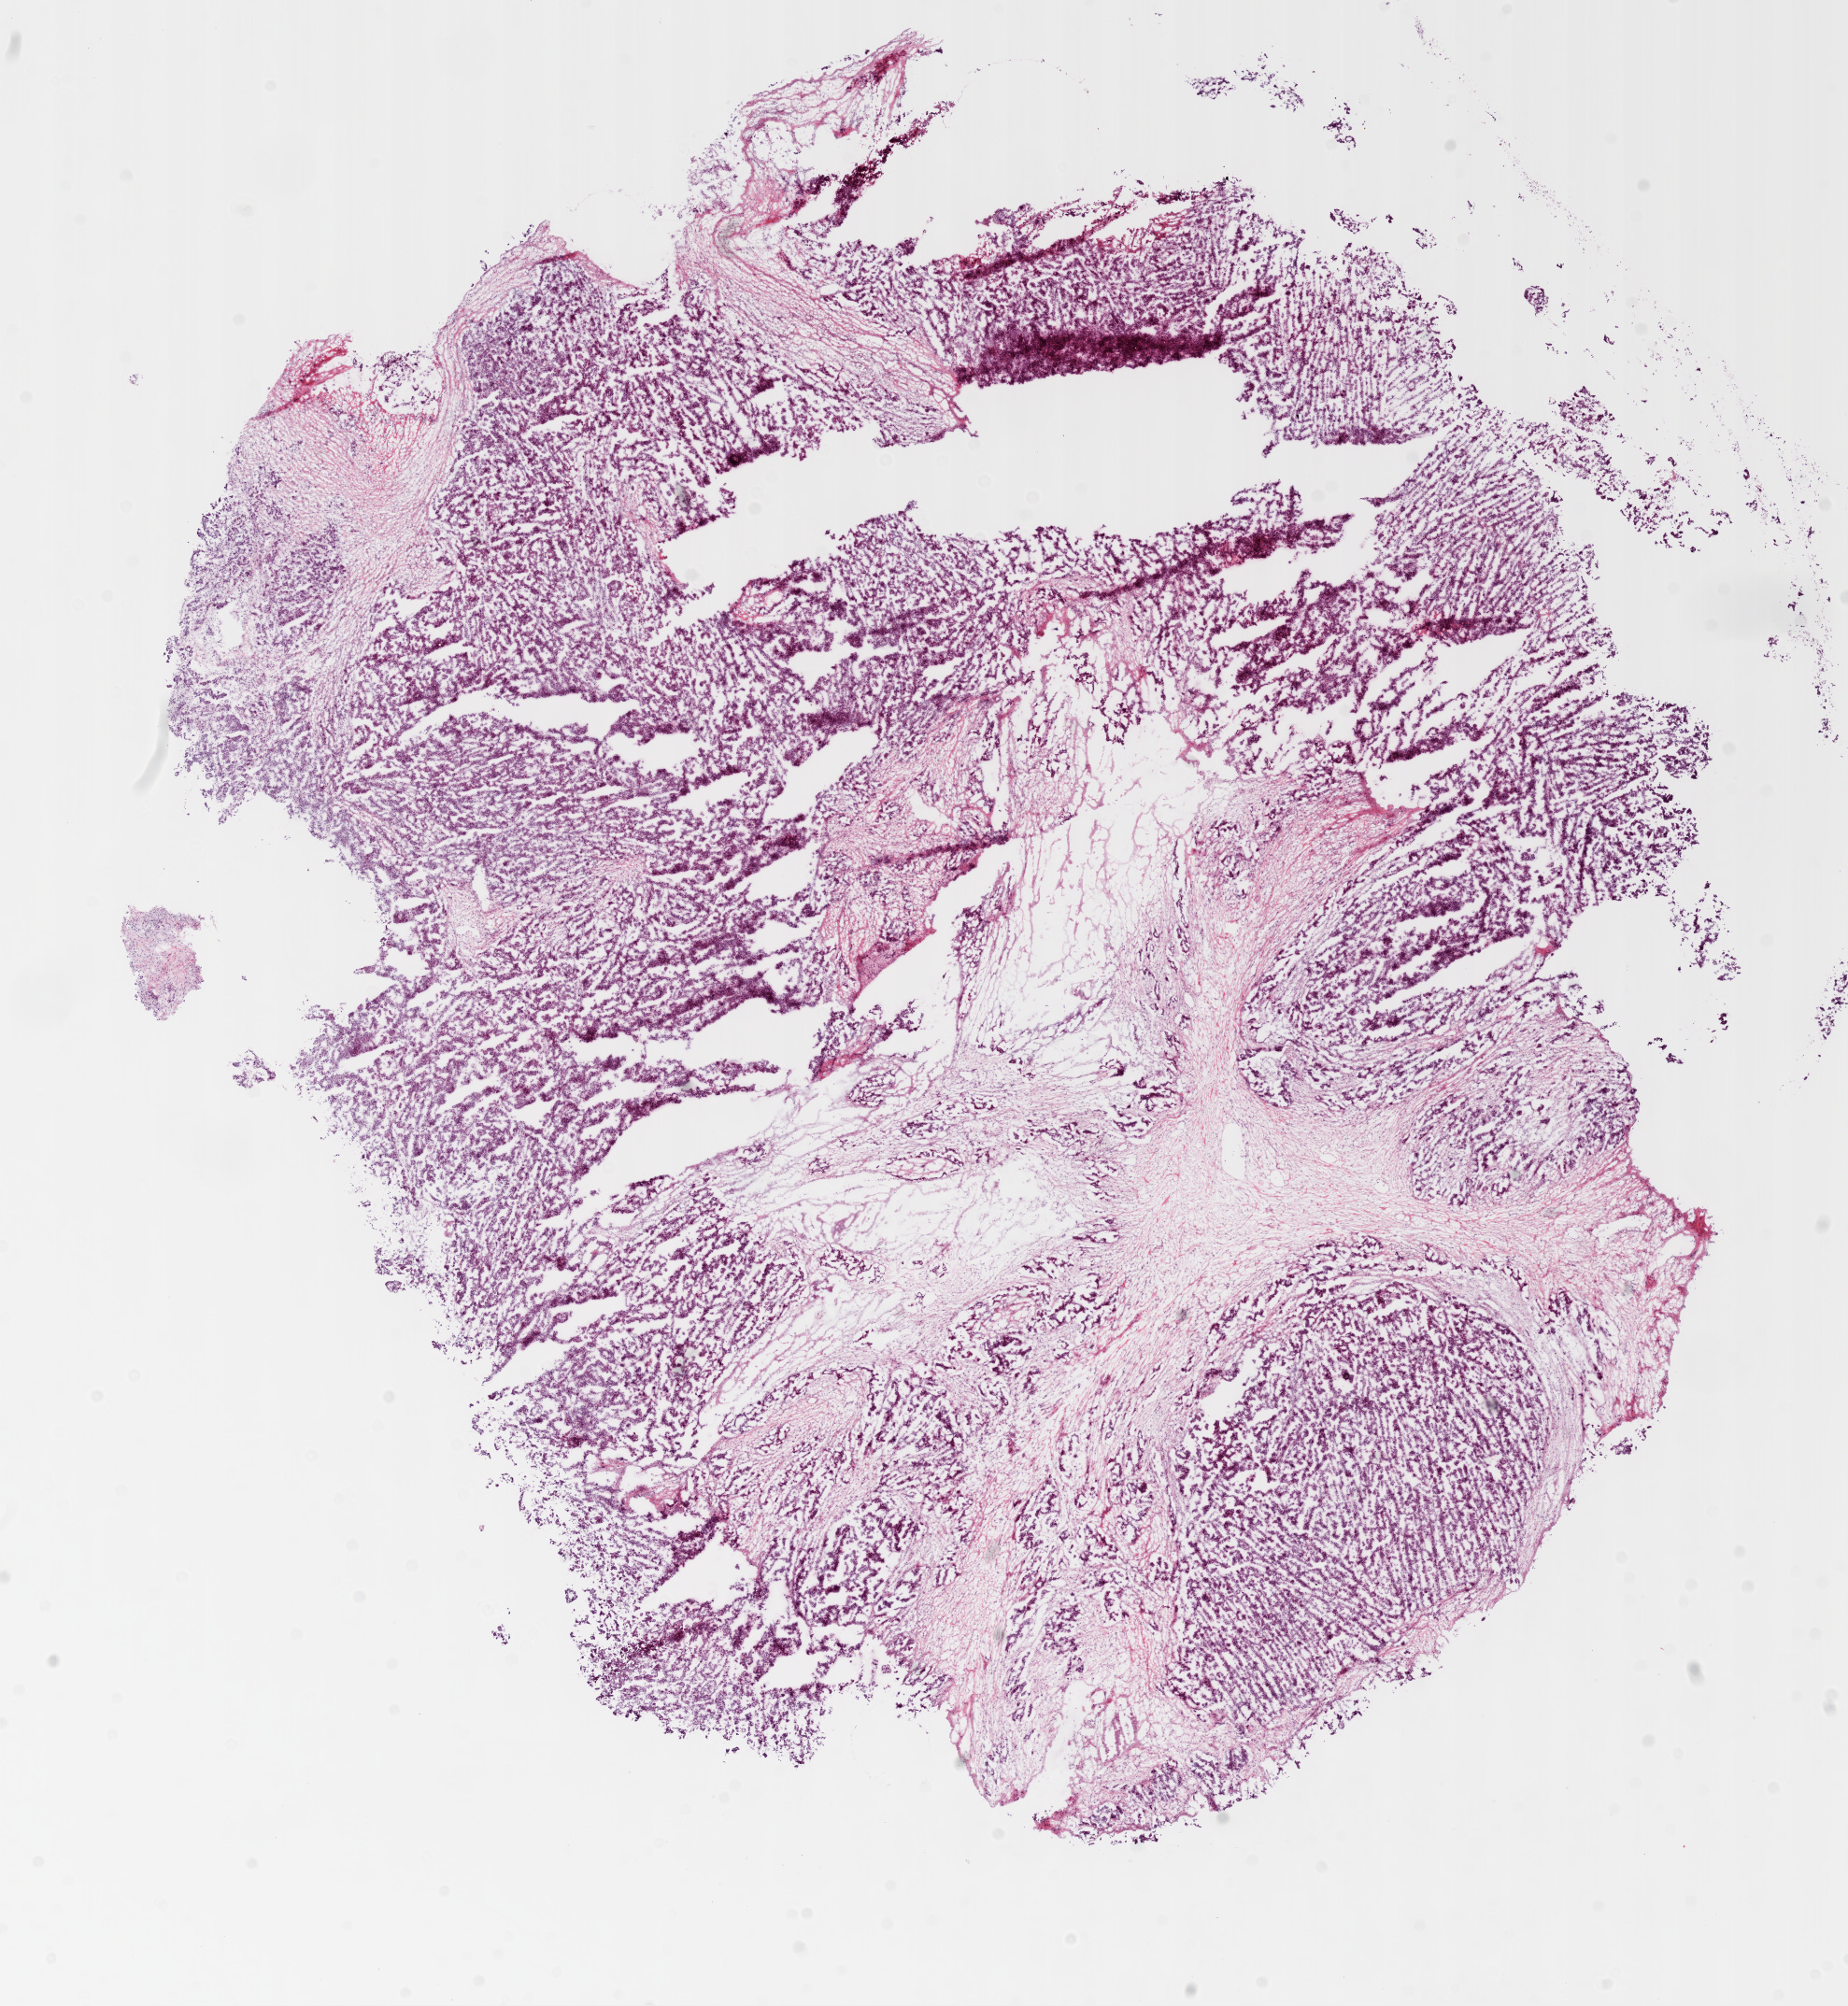
Digitized H&E-stained tissue section (whole slide) — low-resolution overview of the scanned area, about 16.0 x 17.3 mm; frozen section from the top of the tissue portion; primary tumour sample from the ovary. Female patient; age at initial diagnosis 55 years. Histologic grade: GX (grade cannot be assessed). Slide review estimates, as recorded: tumour cells 70%, tumour nuclei 90%, normal cells 0%, stromal cells 30%, necrosis 0%. Inflammatory infiltration, as recorded: lymphocyte infiltration 50%, neutrophil infiltration 50%.
Laterality: bilateral. Diagnosis: Serous cystadenocarcinoma, NOS. FIGO stage: IIIC.